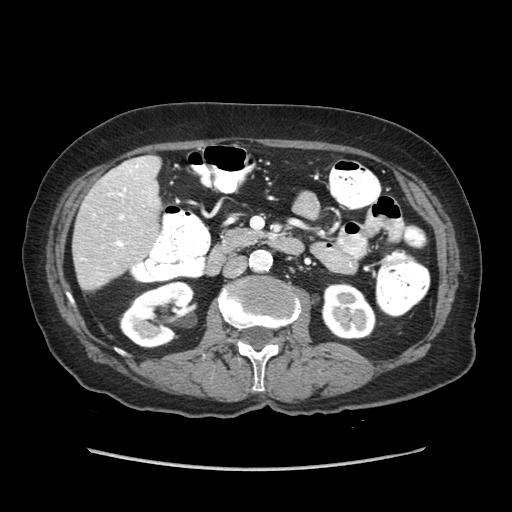
Contrast-enhanced abdominal CT (liver protocol), one axial slice; slice 21 of 89 in the series (ordered by position); reconstruction kernel STANDARD; 140 kVp; soft-tissue window (W 400 / L 40 HU); 2.5 mm slice thickness; 512 × 512 image matrix, field of view 360 × 360 mm. From the clinical record (not read from this slice): diagnosis: hepatocellular carcinoma (patient treated with transarterial chemoembolisation; whether this scan precedes or follows treatment is not stated here); TNM stage (as recorded): Stage-IIIA; Child-Pugh class: A; tumour differentiation: well differentiated.
Structures marked on this image (semi-automatic segmentation, software-assisted and operator-edited):
- liver parenchyma outside the tumour (the mass and vessels are separate outlines, so this box may not span the whole liver): bounding box (x1, y1, x2, y2) in pixels: (72, 156, 160, 290)
- liver vessels: (93, 164, 139, 247)